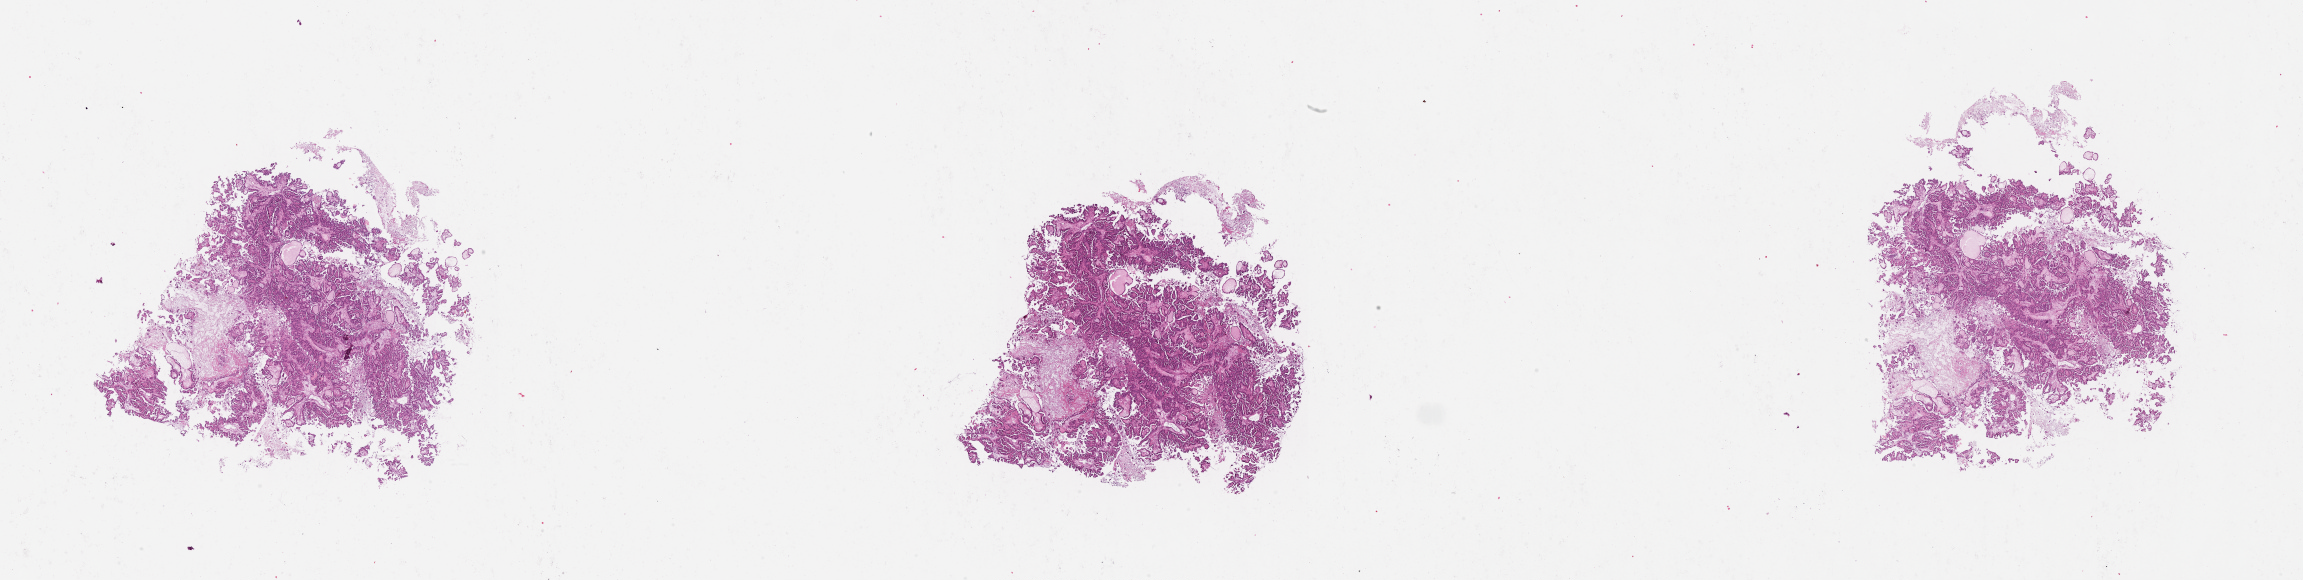
Whole-slide histology image, H&E-stained — low-resolution overview of the scanned area, about 37.1 x 9.3 mm; tumour tissue sample, sampled site: uterus. Female, 66 y/o. Histologic grade: G3 (poorly differentiated). Pathologist review of this section (percent, as recorded): tumour nuclei 80%, necrosis 0%.
AJCC pathologic stage: II. Histologic diagnosis: Endometrioid adenocarcinoma, NOS. Primary tumour site (as recorded): anterior endometrium.